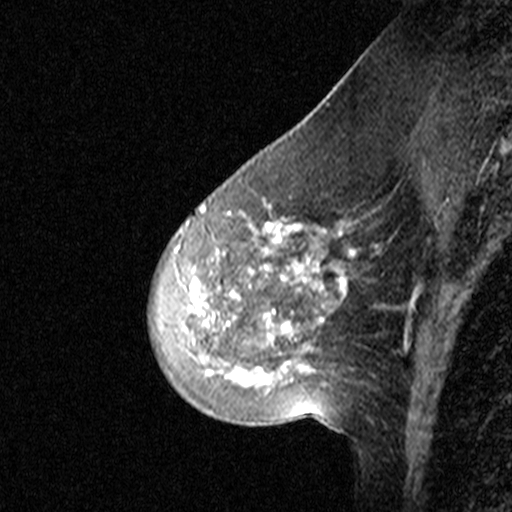
Breast MRI (dynamic contrast-enhanced), one sagittal slice. Position 14 of 44 along the scan axis. Dynamic contrast-enhanced study with each time point stored as its own series, time point 2 of 3 at this slice position (early post-contrast, ordered by acquisition time). 1.5 T. TE 4.5 ms, TR 11 ms. 3 mm slice thickness. 512 × 512 image matrix. Female patient, age 46 years. Case-level facts recorded for this patient, not image findings: setting: breast cancer imaged before/during neoadjuvant chemotherapy; receptor status: HER2-positive.
Annotated regions visible in this slice (semi-automatically segmented with operator editing):
- analysis volume of interest (the breast-tissue region the enhancement analysis was run in; not a lesion): box from (x=146, y=172) to (x=359, y=393) px
- tumour enhancement mask (voxels above the 90 % enhancement threshold inside the analysis volume of interest): (x=185, y=197)–(x=347, y=381)